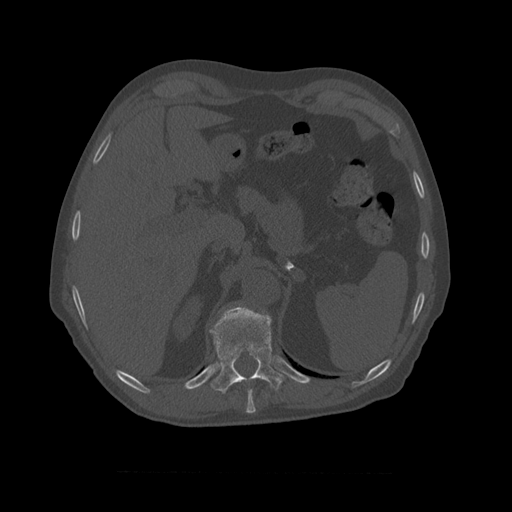
CT including the spine, one axial slice. Position 404 of 450 along the scan axis. 120 kVp. Bone window (W 1800 / L 400 HU). 512 × 512 image matrix, field of view 405 × 405 mm. Patient age 75 years. From the clinical record (not read from this slice): primary cancer: prostate.
Outlined on this slice (semi-automatically segmented with operator editing):
- T10 vertebra: bounding box <209,306,285,394> (left, top, right, bottom; pixels)
- T9 vertebra: <247,389,256,411>